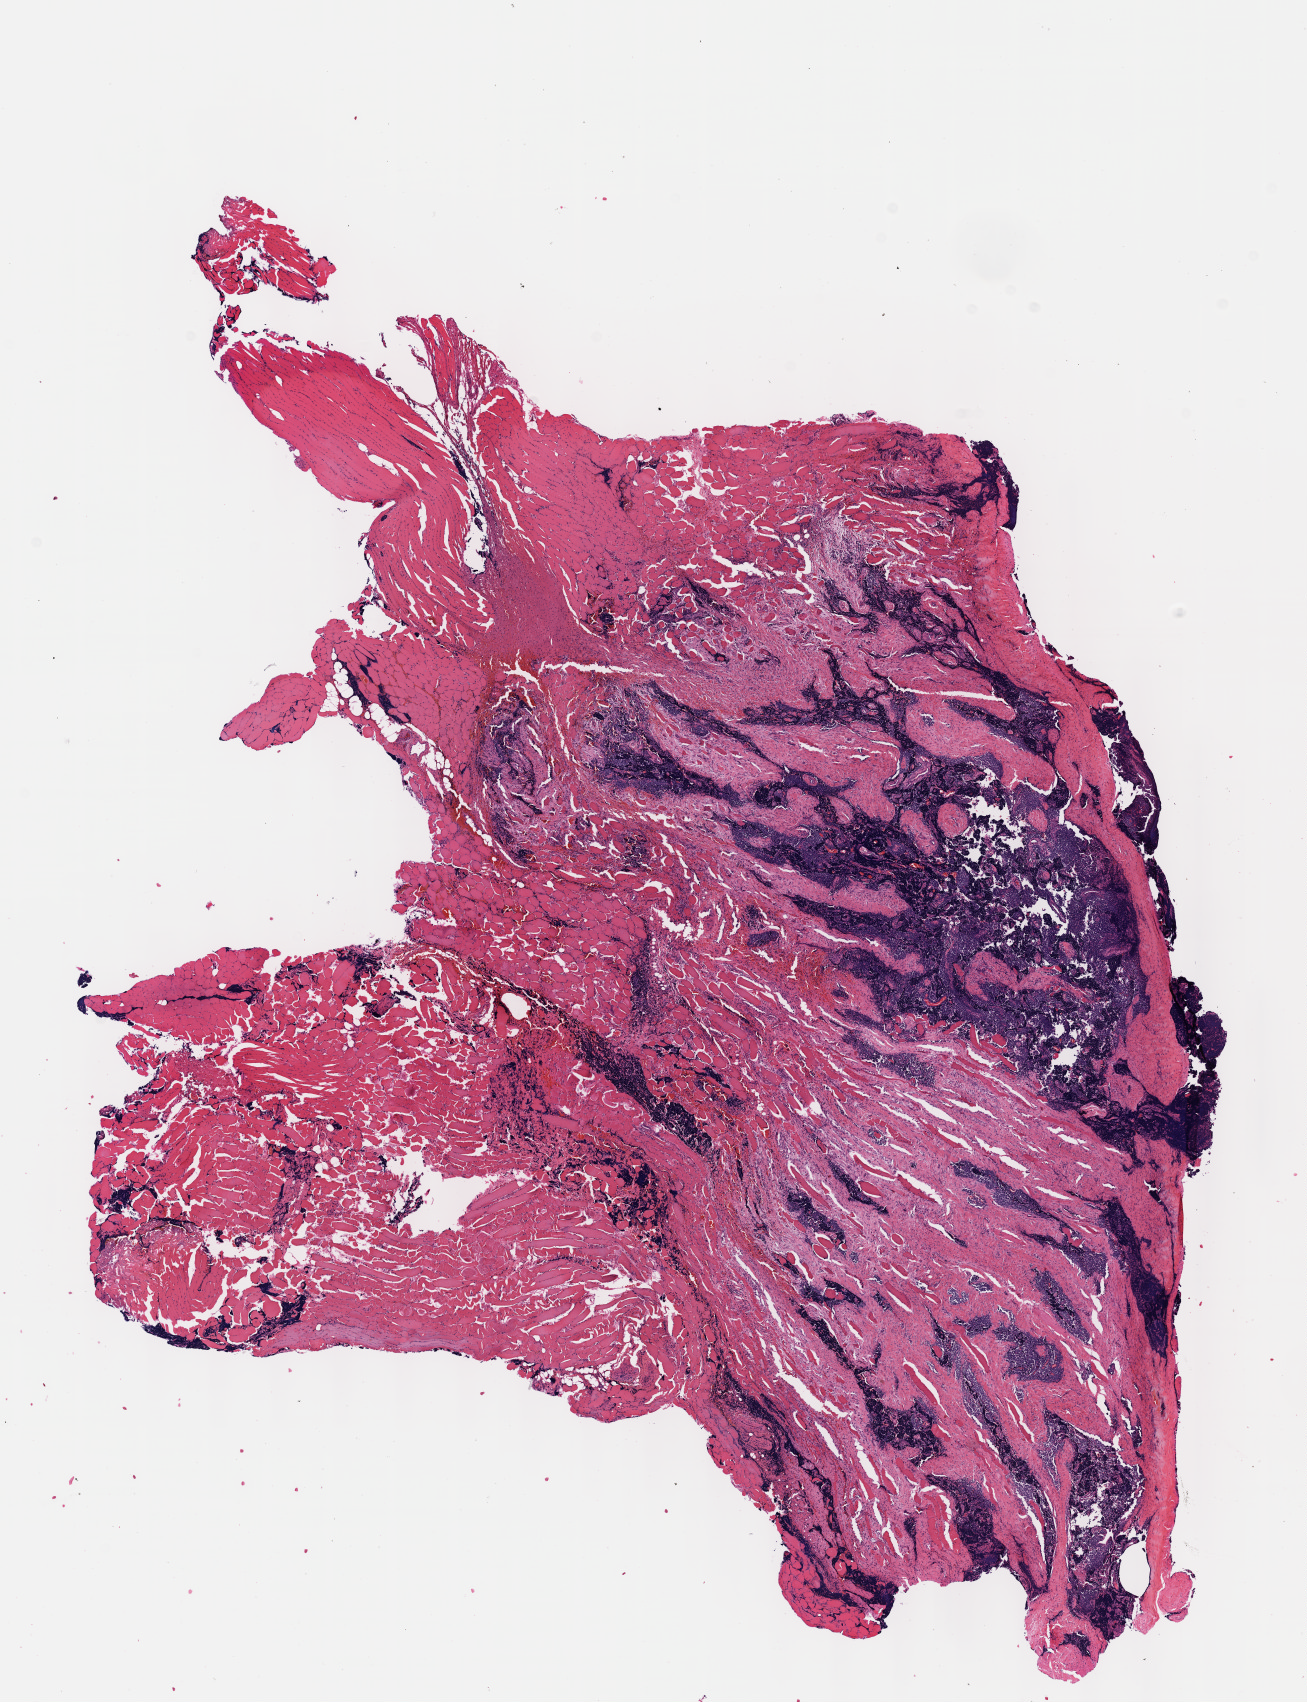
Digitized Hematoxylin and eosin (H&E) stained tissue section (whole slide) — a low-resolution overview of the entire scanned area, about 10.6 x 13.8 mm (from a 40x scan), FFPE section, sample: primary tumour, connective, subcutaneous and other soft tissues. Female, age 35 years at initial diagnosis.
* diagnosis: Synovial sarcoma, NOS (connective, subcutaneous and other soft tissues of upper limb and shoulder)